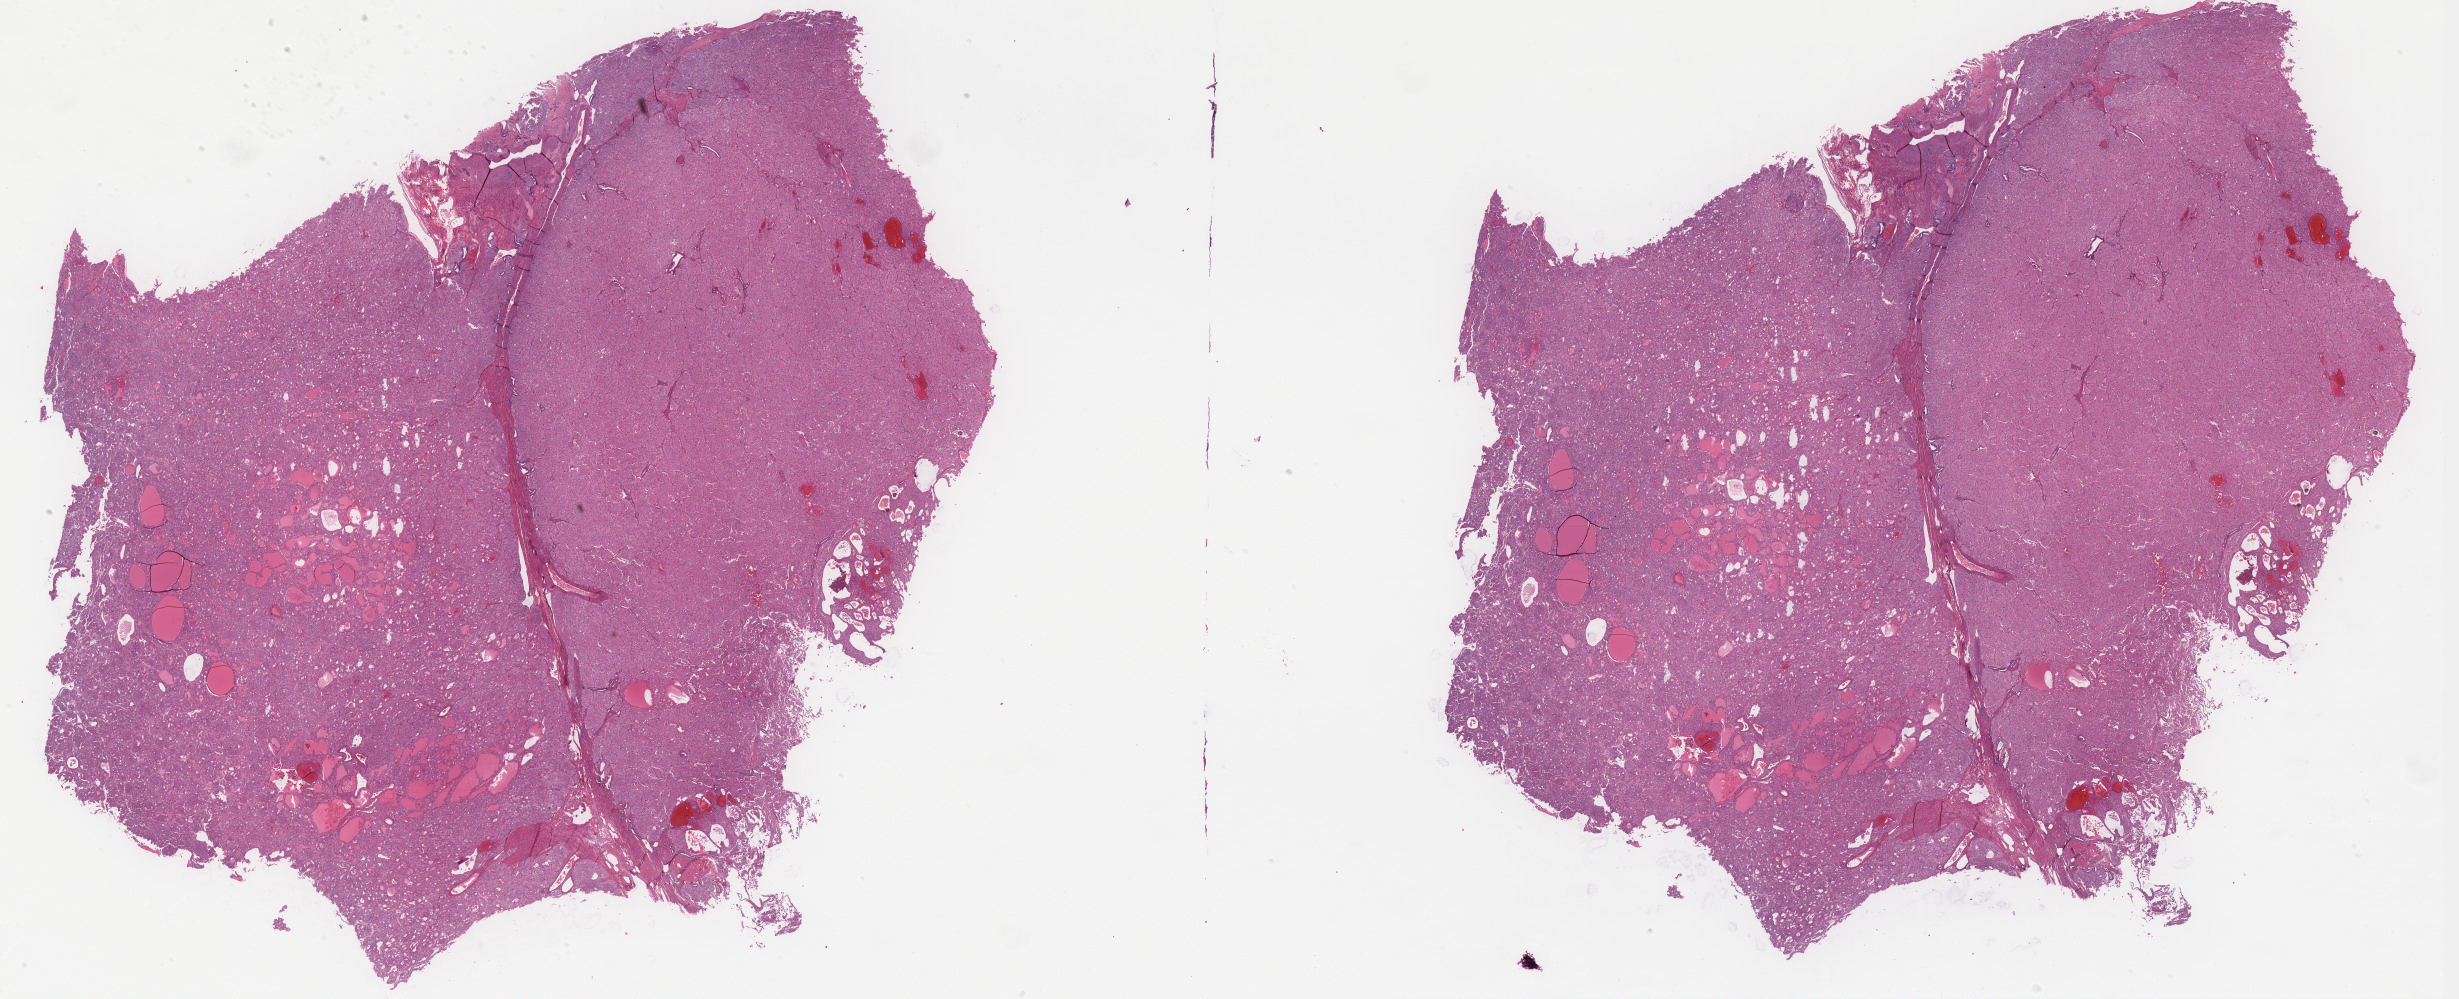
Hematoxylin and eosin (H&E) stained whole-slide image — low-resolution overview of the scanned area, about 39.3 x 16.0 mm (acquisition: 40x scan); formalin-fixed paraffin-embedded (FFPE) diagnostic section; kidney, primary tumour sample. Male patient; age at initial diagnosis 72 years.
Laterality: right. AJCC pathologic stage: III. Diagnosis: Renal cell carcinoma, chromophobe type.